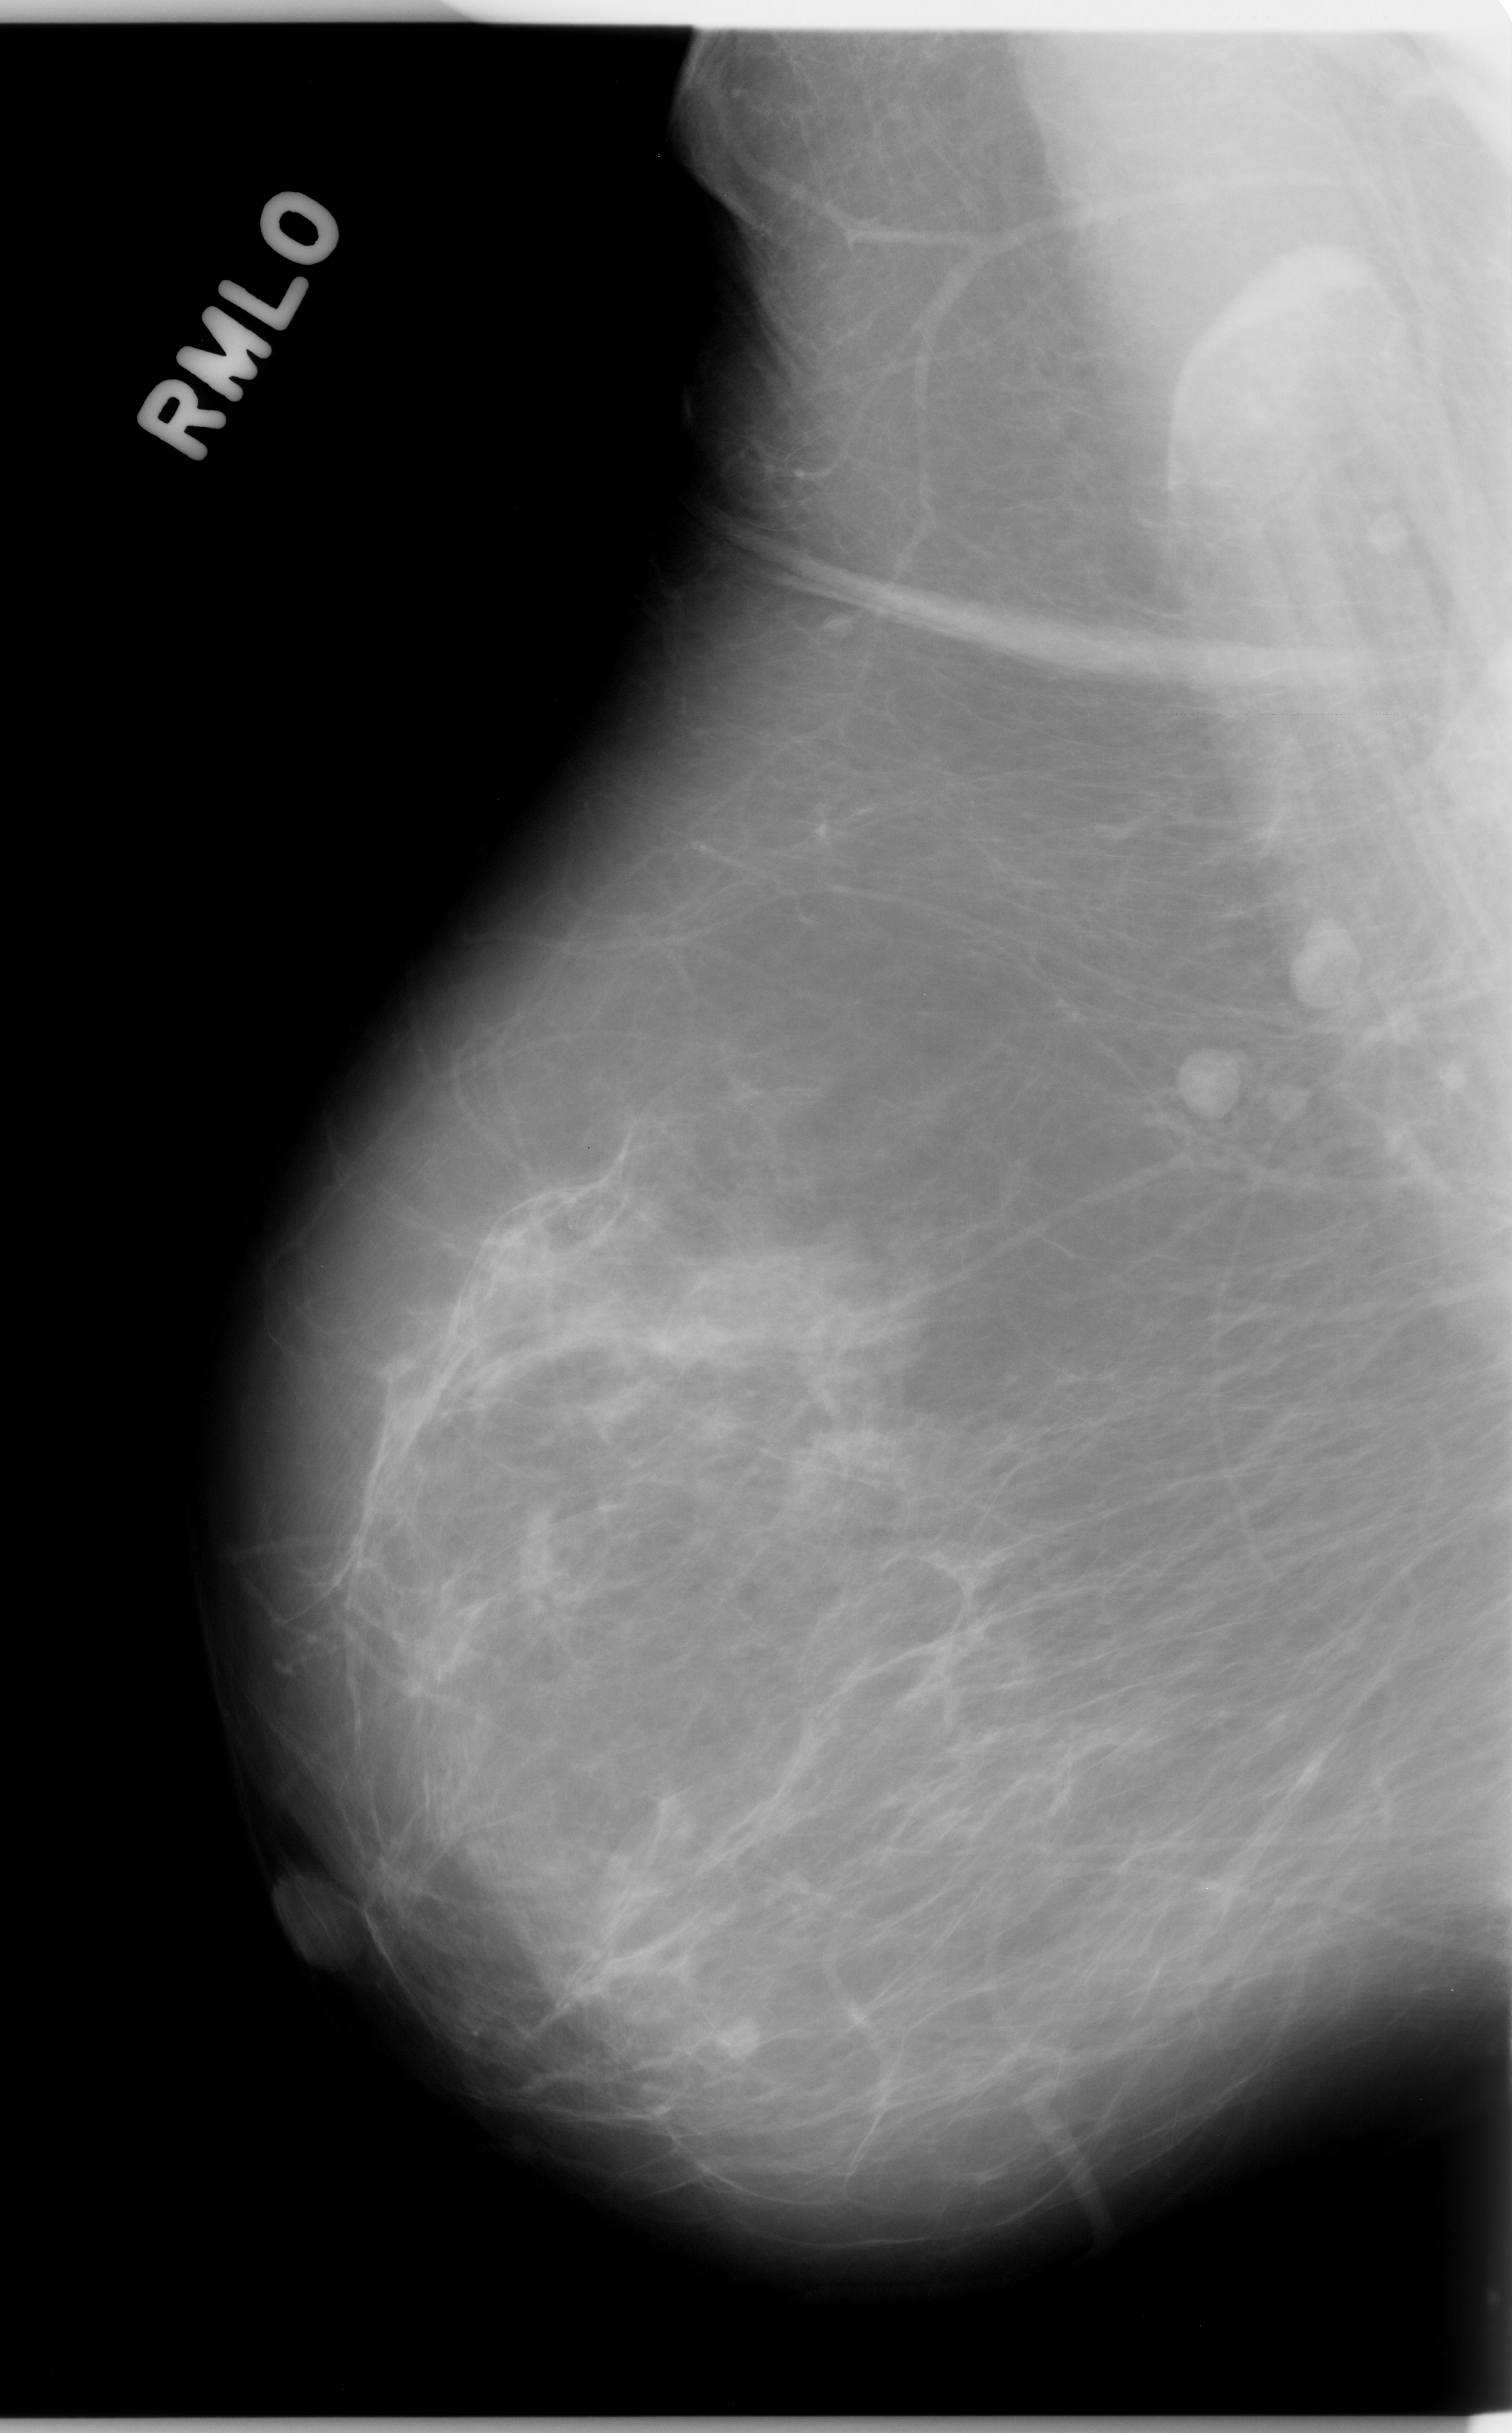
Mammogram (digitized film); right breast; MLO view; BI-RADS breast density category 1 (scale 1–4); 1512 × 2433 image matrix.
Marked abnormalities (boxes around the expert regions of interest):
- calcifications, morphology punctate, distribution clustered; BI-RADS assessment category 4; pathology (as recorded): benign: bounding box [x1, y1, x2, y2] px = [691, 1987, 798, 2092]